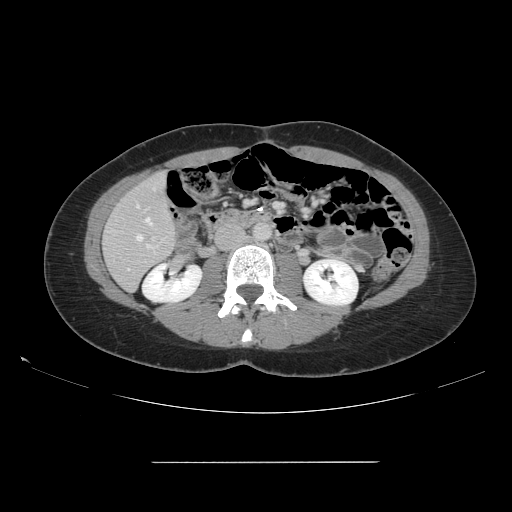
Contrast-enhanced abdominal CT, one axial slice; slice 50 of 151 in the series (ordered by position); intravenous contrast given; soft-tissue window (W 400 / L 40 HU); 512 × 512 image matrix, field of view 421 × 421 mm. Female patient, age 46 years. From the clinical record (not read from this slice): diagnosis: colorectal cancer liver metastases, imaged before liver resection; multiple liver metastases: yes; largest metastasis: 3 cm.
Structures marked on this image (manually delineated by an expert):
- hepatic veins: box from (x=137, y=218) to (x=152, y=240) px
- liver: (x=105, y=174)–(x=176, y=290)
- planned liver remnant (the part of the liver to remain after resection): (x=105, y=174)–(x=176, y=290)